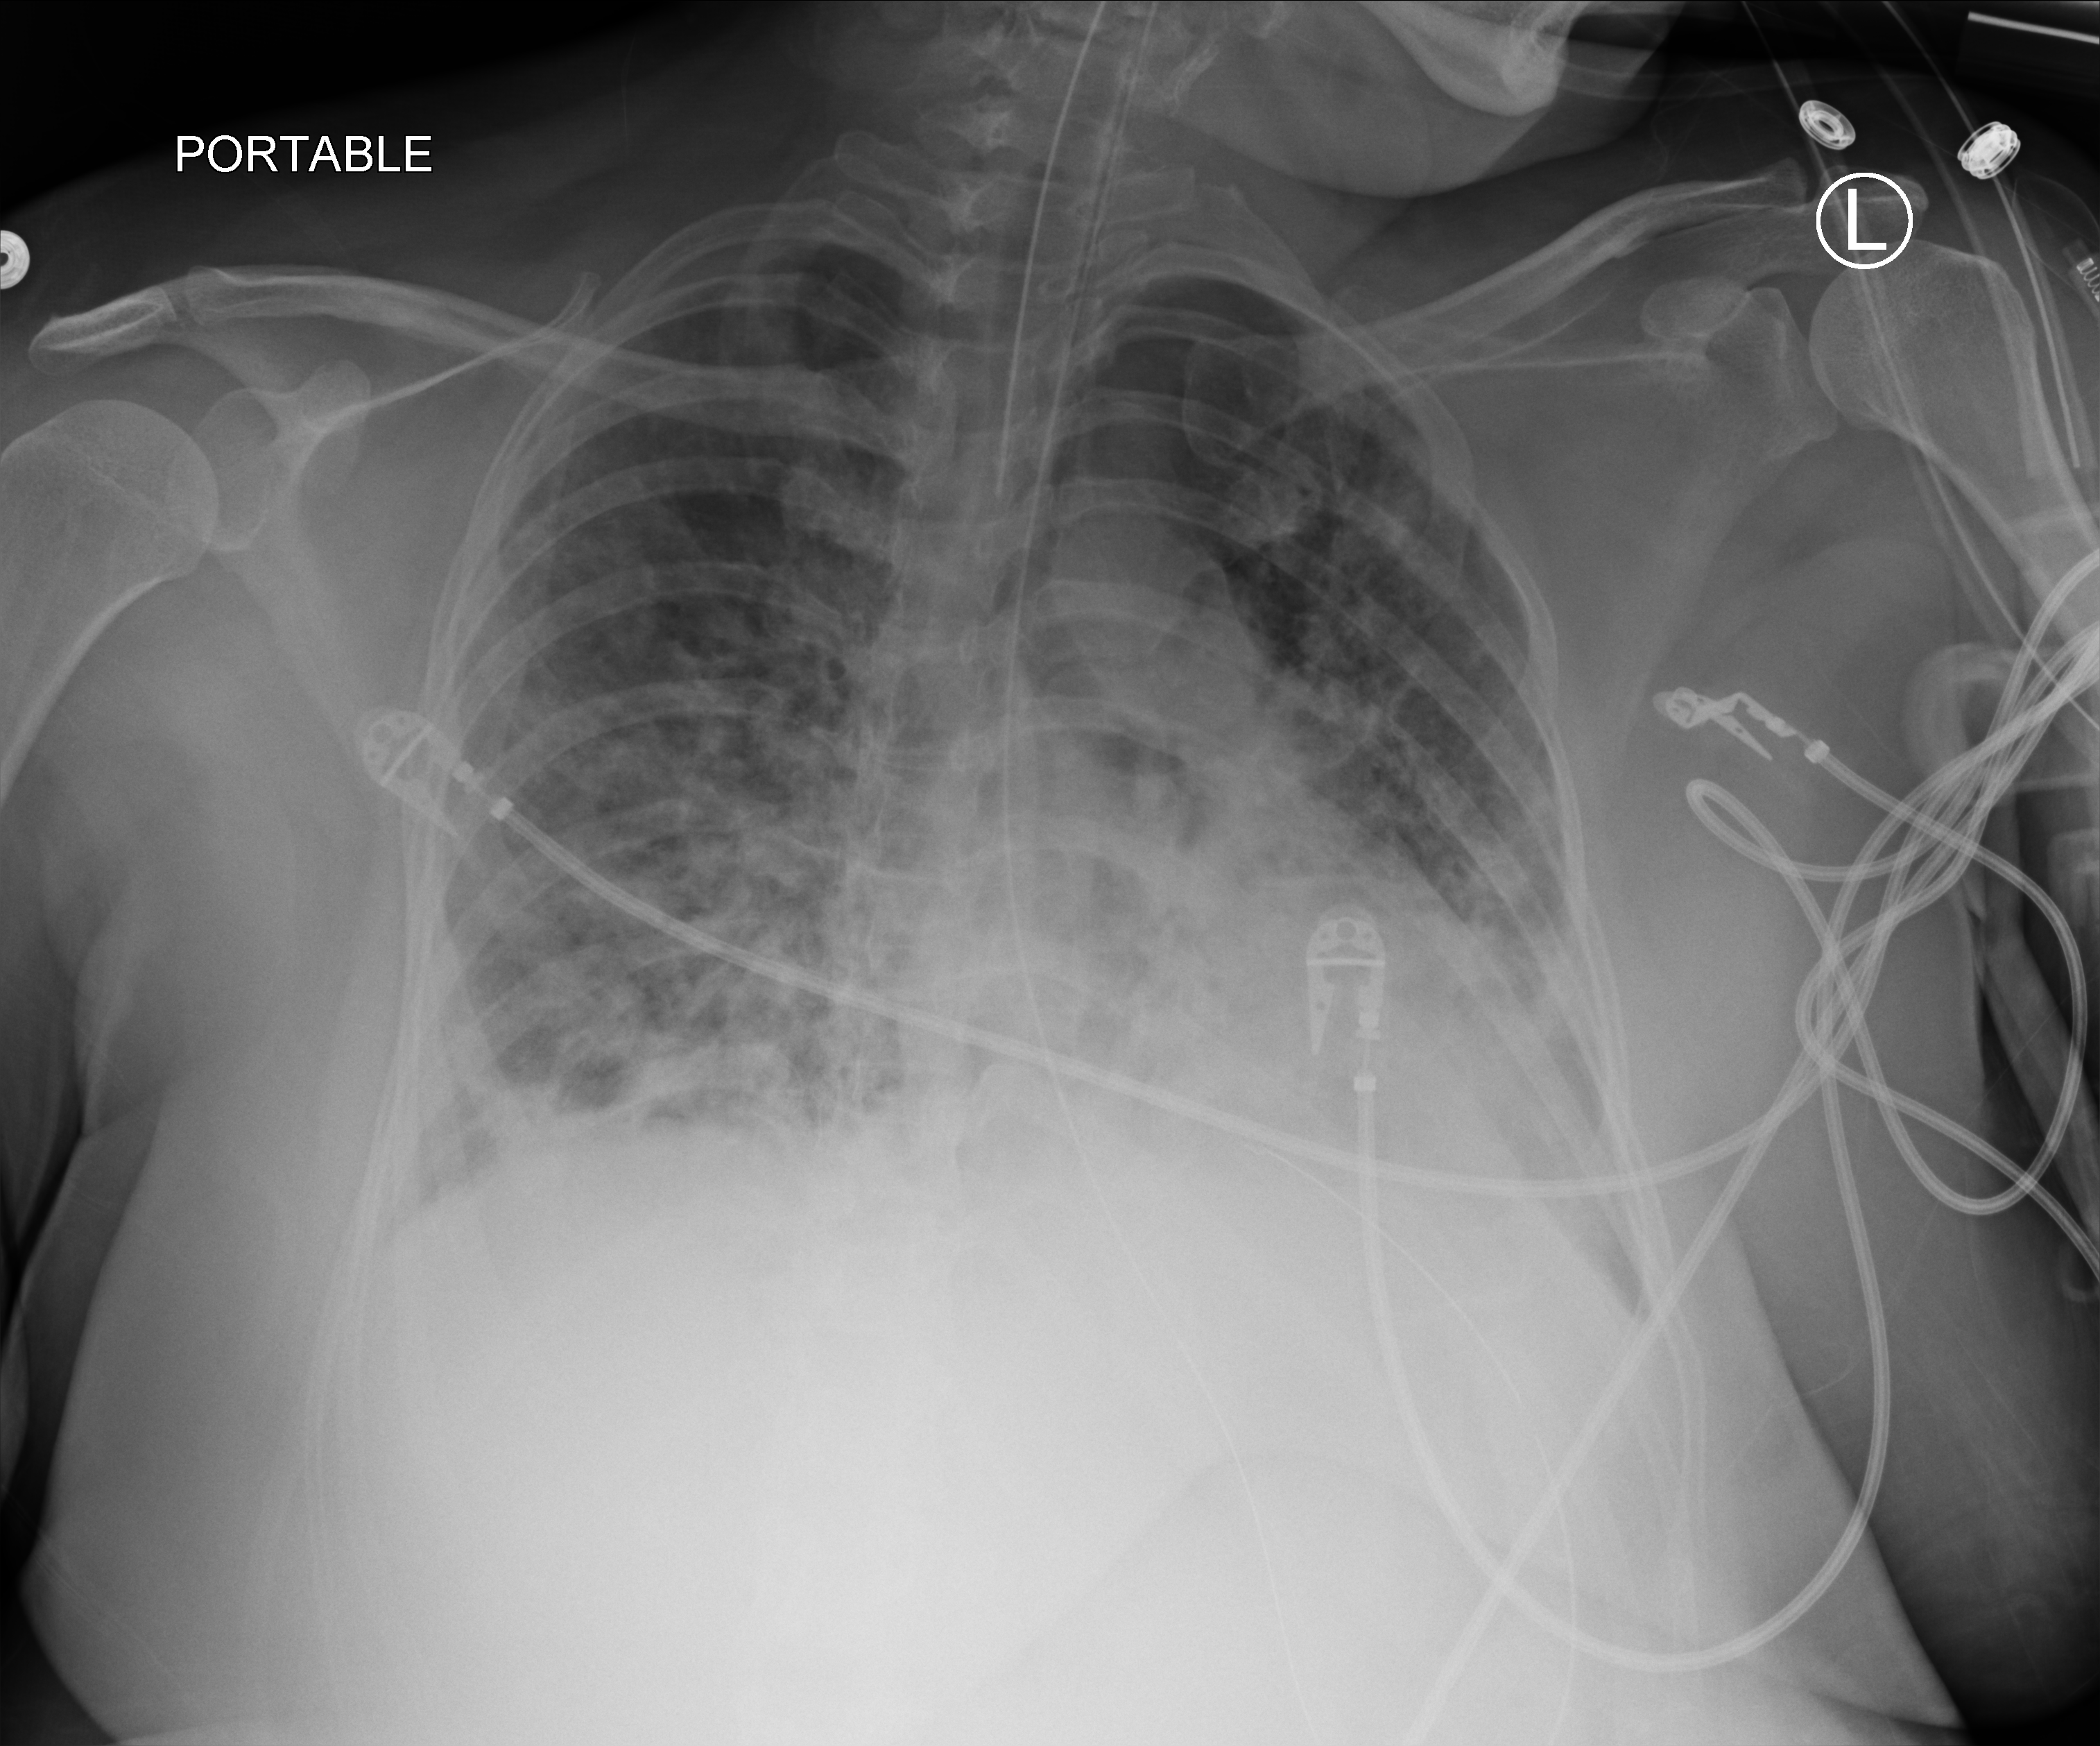
Bedside chest radiograph (computed radiography). Patient hospitalised with COVID-19, aged 18–59 years.
From the hospital-stay record, not from the radiograph (when in the stay this image was taken is not recorded): COPD (admission record): no; admitted to intensive care during this hospital stay: yes.